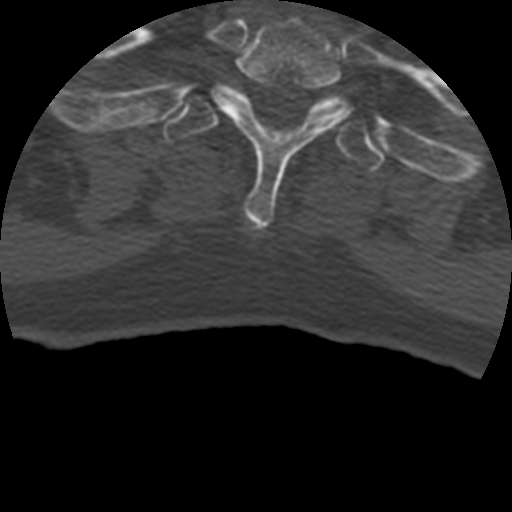
CT including the spine, one axial slice. Position 378 of 399 along the scan axis. Bone window (W 1800 / L 400 HU). 512 × 512 image matrix. Patient age 69 years. Case-level facts recorded for this patient, not image findings: primary cancer: prostate.
Outlined on this slice (semi-automatically segmented with operator editing):
- T1 vertebra: bounding box [x1, y1, x2, y2] px = [209, 19, 352, 228]
- T2 vertebra: [162, 83, 385, 171]